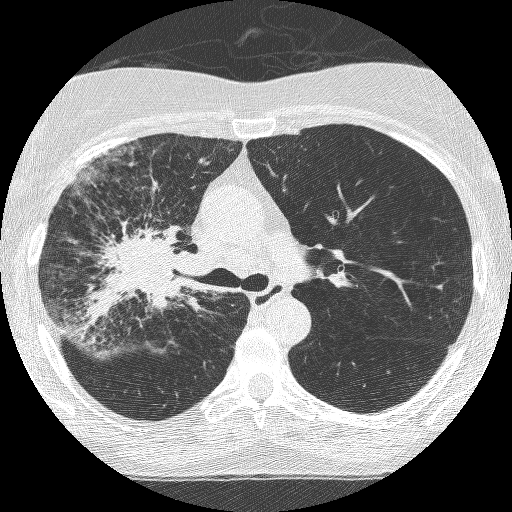
Chest CT (low-dose screening protocol), one axial image. Third screening round (two years after baseline). Lung window (W 1500 / L -600 HU). 1.25 mm slice thickness. 120 kVp. Slice 170 of 253 in the series. Female, age 64 years at enrolment.
- Expert-annotated lung lesion, bounding box <86,214,205,333> (left, top, right, bottom; pixels).
- Reader record for this screening exam (exam-level; its link to the box is not recorded): non-calcified nodule or mass ≥4 mm, right upper lobe, 49 × 43 mm, spiculated (stellate) margins, soft tissue attenuation, pre-existing on the prior screen: yes; interval growth: yes.